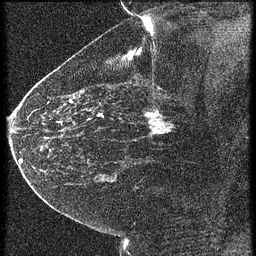
Breast MRI (dynamic contrast-enhanced), one sagittal slice; slice 36 of 60 in the series (ordered by position); 4 images stored at this slice position (order not interpretable as contrast timing); 1.5 T; TE 4.2 ms, TR 21.3 ms; 1.5 mm slice thickness; 256 × 256 image matrix, field of view 180 × 180 mm. Female patient, age 43 years. Case-level facts recorded for this patient, not image findings: setting: breast cancer imaged before/during neoadjuvant chemotherapy; receptor status: HER2-positive.
Outlined on this slice (semi-automatic segmentation, software-assisted and operator-edited):
- analysis volume of interest (the breast-tissue region the enhancement analysis was run in; not a lesion): bounding box (x1, y1, x2, y2) in pixels: (122, 100, 187, 151)
- tumour enhancement mask (voxels above the 90 % enhancement threshold inside the analysis volume of interest): (146, 112, 173, 135)